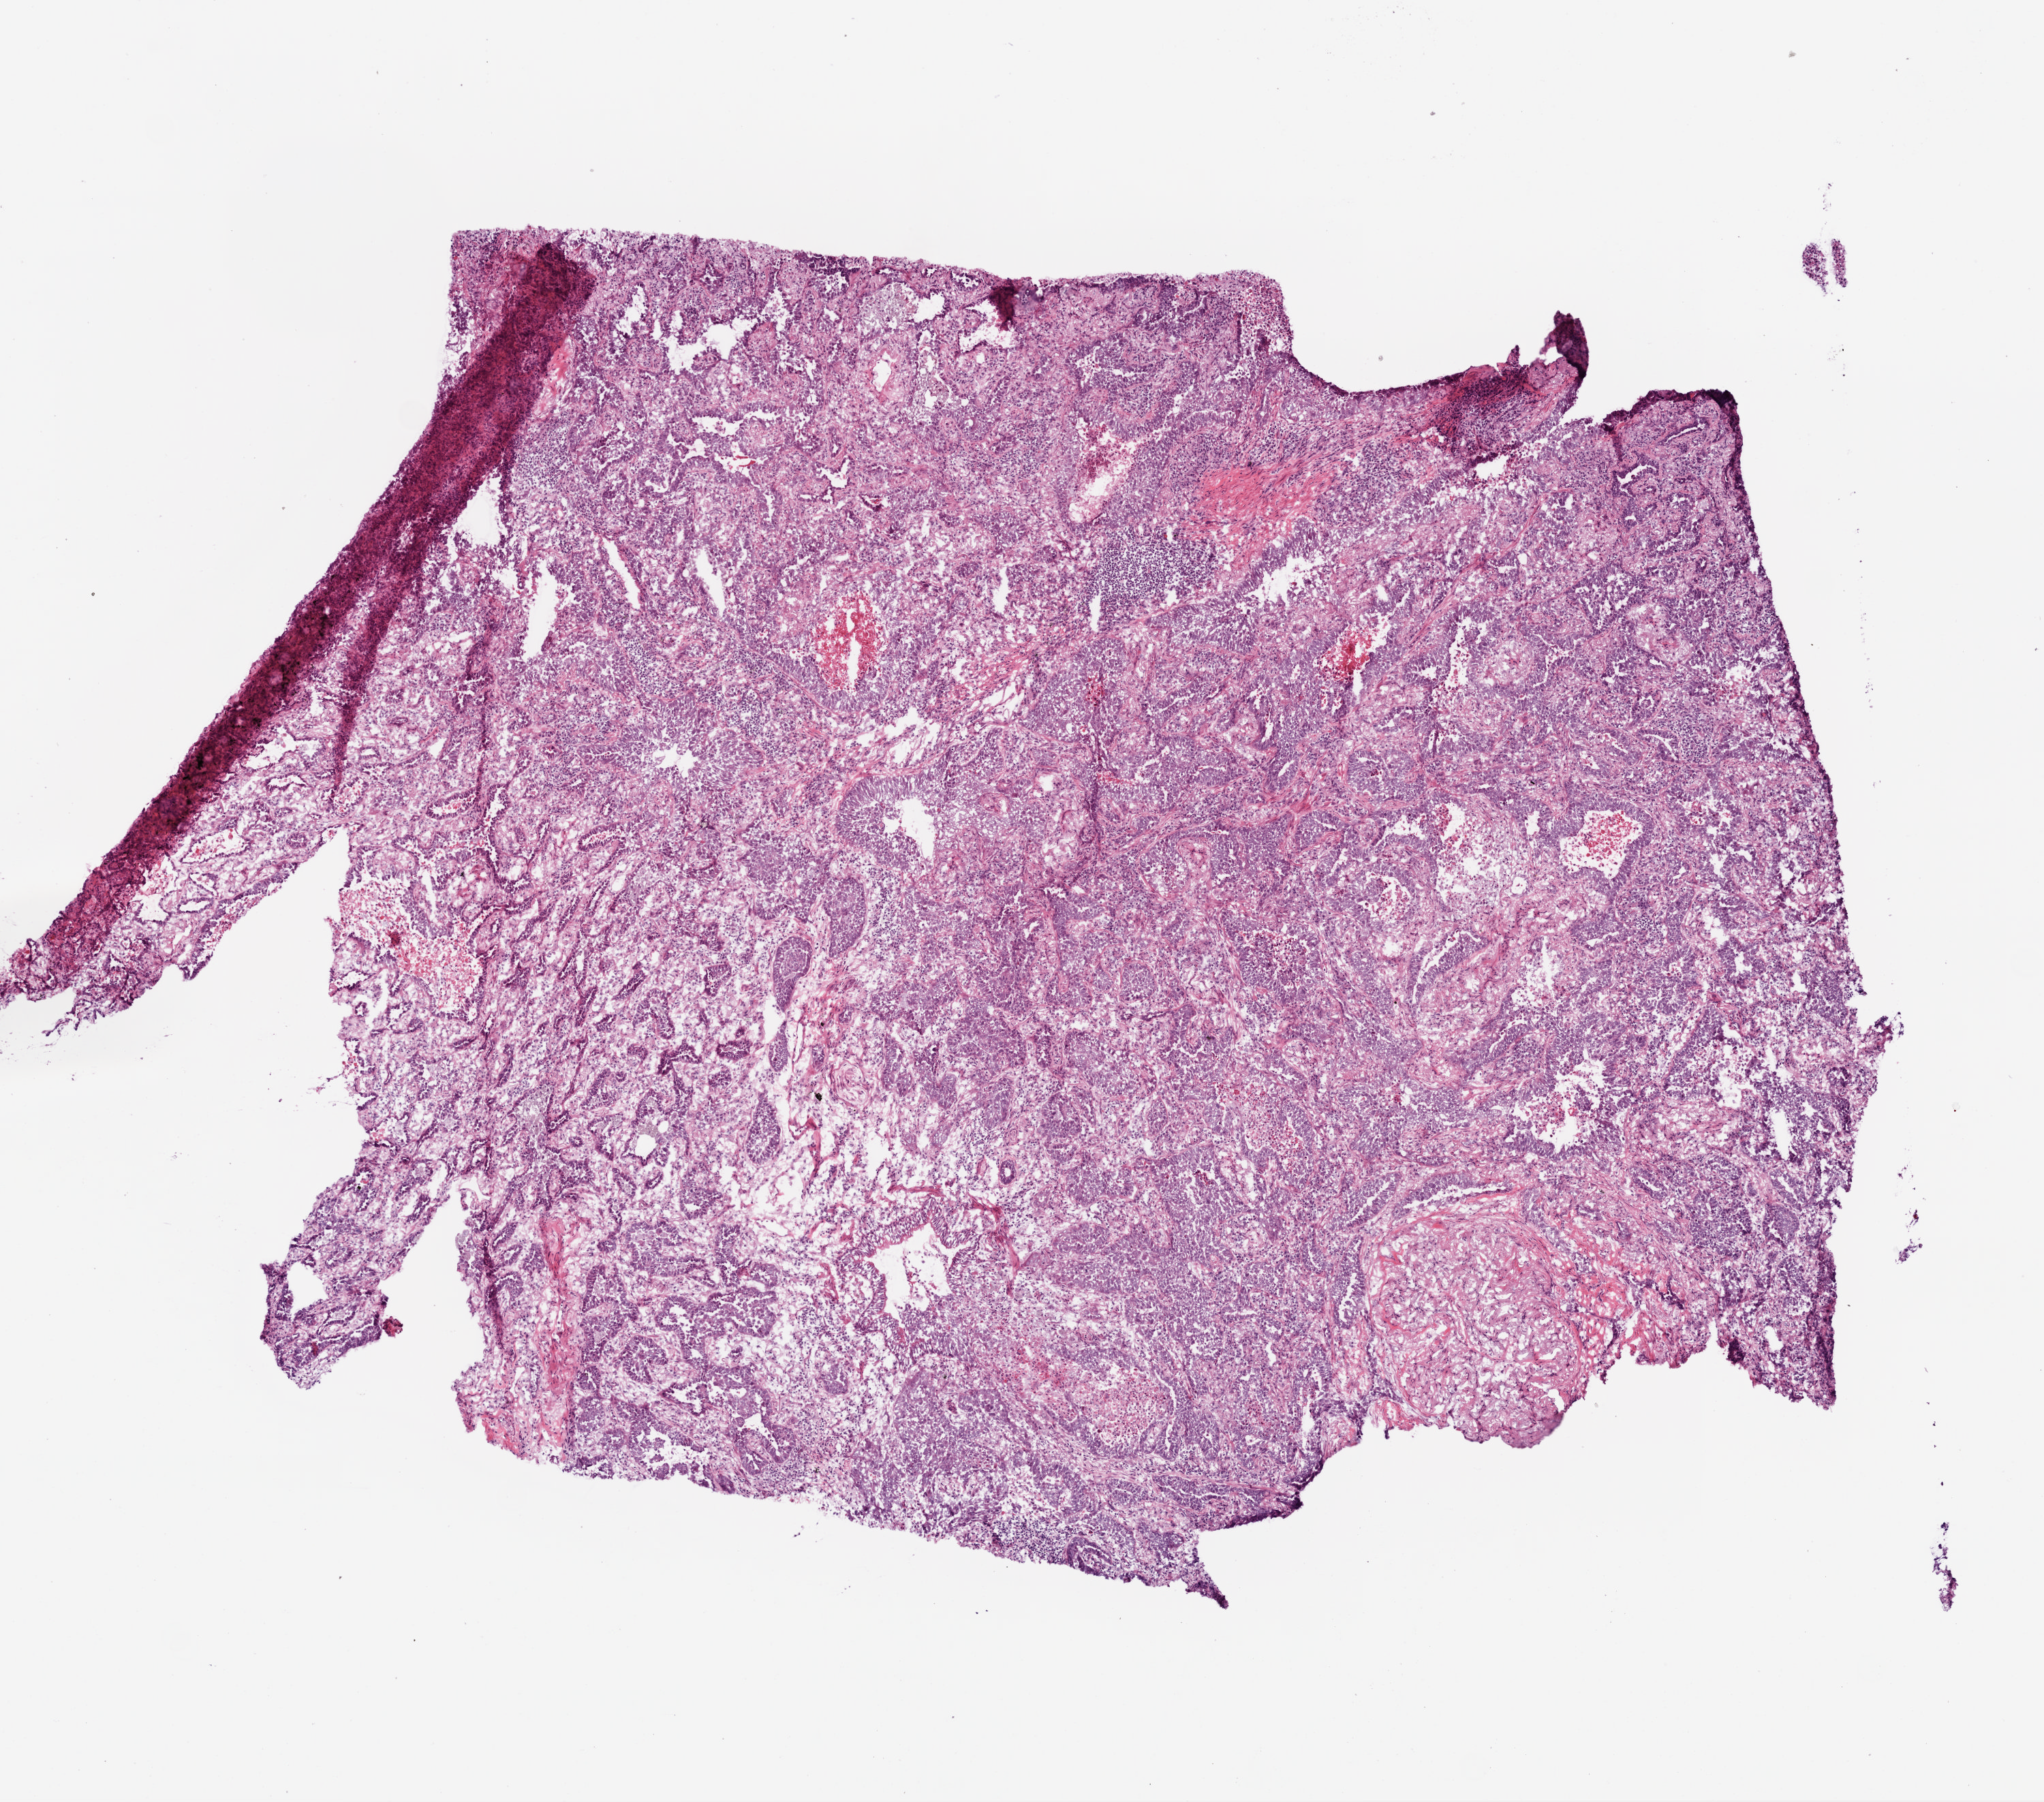
Whole-slide histology image, Hematoxylin and eosin (H&E) stained — low-resolution overview of the scanned area, about 6.0 x 5.3 mm; frozen section from the top of the tissue portion; sample: primary tumour, lung. Female patient. Pathologist review of this section (percent, as recorded): tumour cells 80%, tumour nuclei 70%, normal cells 0%, stromal cells 15%, necrosis 5%.
Pathologic diagnosis: Bronchiolo-alveolar carcinoma, non-mucinous (upper lobe, lung). AJCC pathologic stage: IB (6th edition).